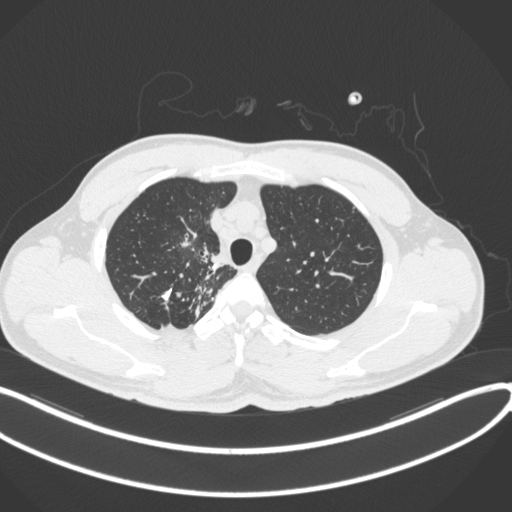
Chest CT, one axial slice. Position 301 of 391 along the scan axis. 120 kVp. Lung window (W 1500 / L -600 HU). 1 mm slice thickness. 512 × 512 image matrix. Patient: male, 48 years. Case-level facts recorded for this patient, not image findings: clinical TNM (as recorded): T1c N1 M1.
Annotated regions visible in this slice (rectangle marked by the reading radiologist):
- lung tumour (recorded histology: adenocarcinoma): bounding box <171,222,201,254> (left, top, right, bottom; pixels)